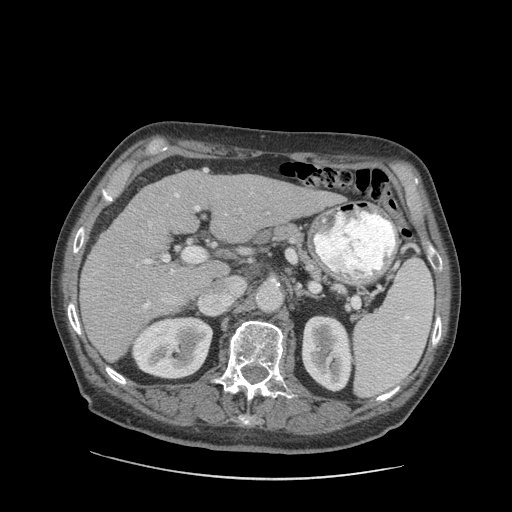
Contrast-enhanced abdominal CT (liver protocol), one axial slice. Position 50 of 89 along the scan axis. 140 kVp. Soft-tissue window (W 400 / L 40 HU). 2.5 mm slice thickness. 512 × 512 image matrix. Case-level facts recorded for this patient, not image findings: diagnosis: hepatocellular carcinoma (patient treated with transarterial chemoembolisation; whether this scan precedes or follows treatment is not stated here); TNM stage (as recorded): Stage-I; Child-Pugh class: A; tumour nodularity: uninodular.
Structures marked on this image (semi-automatic segmentation, software-assisted and operator-edited):
- liver parenchyma outside the tumour (the mass and vessels are separate outlines, so this box may not span the whole liver): bounding box [x1, y1, x2, y2] px = [80, 169, 340, 362]
- liver vessels: [88, 170, 269, 312]